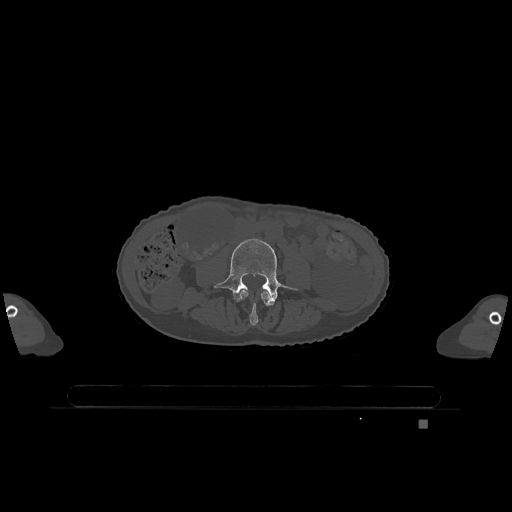
CT including the spine, one axial slice. Slice 313 of 1317 in the series (ordered by position). Bone window (W 1800 / L 400 HU). 0.5 mm slice thickness. 512 × 512 image matrix, field of view 500 × 500 mm. Female patient, age 74 years. From the clinical record (not read from this slice): primary cancer: lung.
Annotated regions visible in this slice (semi-automatic segmentation, software-assisted and operator-edited):
- L3 vertebra: box from (x=239, y=290) to (x=271, y=326) px
- L4 vertebra: (x=213, y=238)–(x=297, y=305)